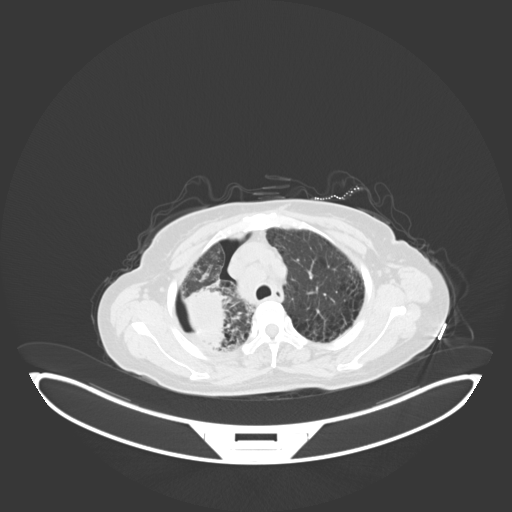
Chest CT, one axial slice; slice 48 of 69 in the series (ordered by position); reconstruction kernel B30f; 120 kVp; lung window (W 1500 / L -600 HU); 3 mm slice thickness; 512 × 512 image matrix, field of view 500 × 500 mm. Female patient, age 64 years. Case-level facts recorded for this patient, not image findings: clinical TNM (as recorded): T3 N3 M0.
Outlined on this slice (rectangle marked by the reading radiologist):
- lung tumour (recorded histology: squamous cell carcinoma): bounding box <179,282,230,357> (left, top, right, bottom; pixels)